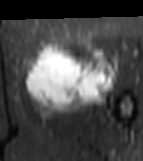
MRI of an extremity soft-tissue mass, one axial slice; slice 30 of 81 in the series (ordered by position); STIR; MR volume resampled by the dataset authors to the PET/CT grid (not the native acquisition matrix); 143 × 161 image matrix, field of view 140 × 157 mm. Female patient. From the clinical record (not read from this slice): histological type: myxofibrosarcoma; grade: intermediate; site of the primary tumour: left thigh.
Structures marked on this image (expert contour drawn on MRI and transferred to this co-registered scan by the dataset authors):
- gross tumour volume including surrounding oedema: box from (x=24, y=46) to (x=118, y=118) px
- gross tumour volume (mass): (x=26, y=44)–(x=114, y=107)